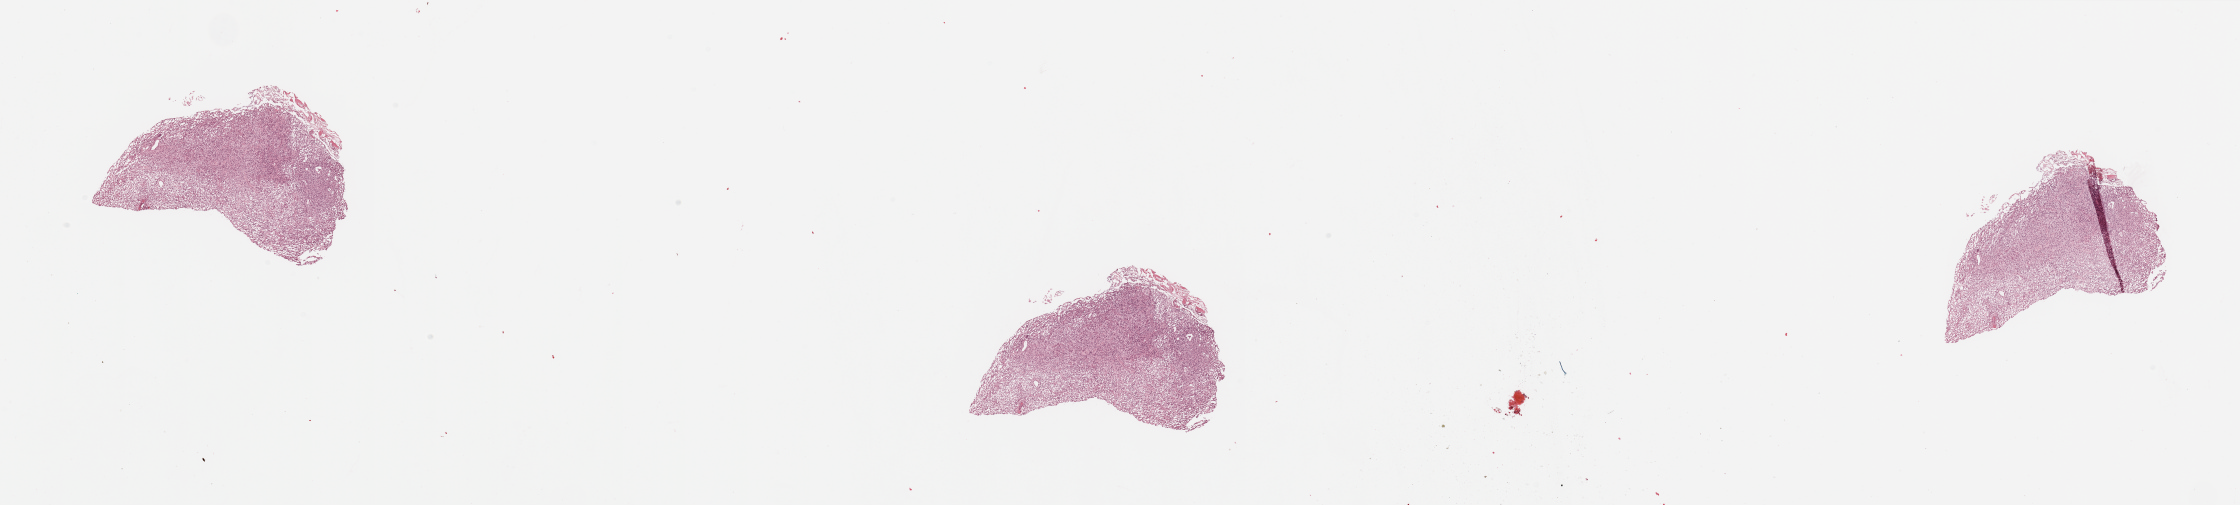
H&E whole-slide image, whole scanned area (about 35.4 x 8.0 mm, slide scanned at 20x) shown as a low-resolution overview, tumour tissue sample, sampled site: brain. 65-year-old male patient. Slide review estimates, as recorded: tumour nuclei 85%, necrosis 0%.
- diagnosis: Glioblastoma
- primary tumour site (as recorded): parietal lobe